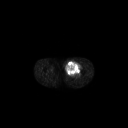
FDG PET of an extremity soft-tissue mass (from a PET/CT study), one axial slice. Slice 239 of 267 in the series (ordered by position). 3.27 mm slice thickness. 128 × 128 image matrix, field of view 700 × 700 mm. Male patient, age 63 years. Case-level facts recorded for this patient, not image findings: histological type: pleiomorphic liposarcoma; grade: high; site of the primary tumour: left thigh.
Outlined on this slice (expert contour drawn on MRI and transferred to this co-registered scan by the dataset authors):
- gross tumour volume including surrounding oedema: box from (x=65, y=60) to (x=82, y=76) px
- gross tumour volume (mass): (x=66, y=60)–(x=81, y=76)